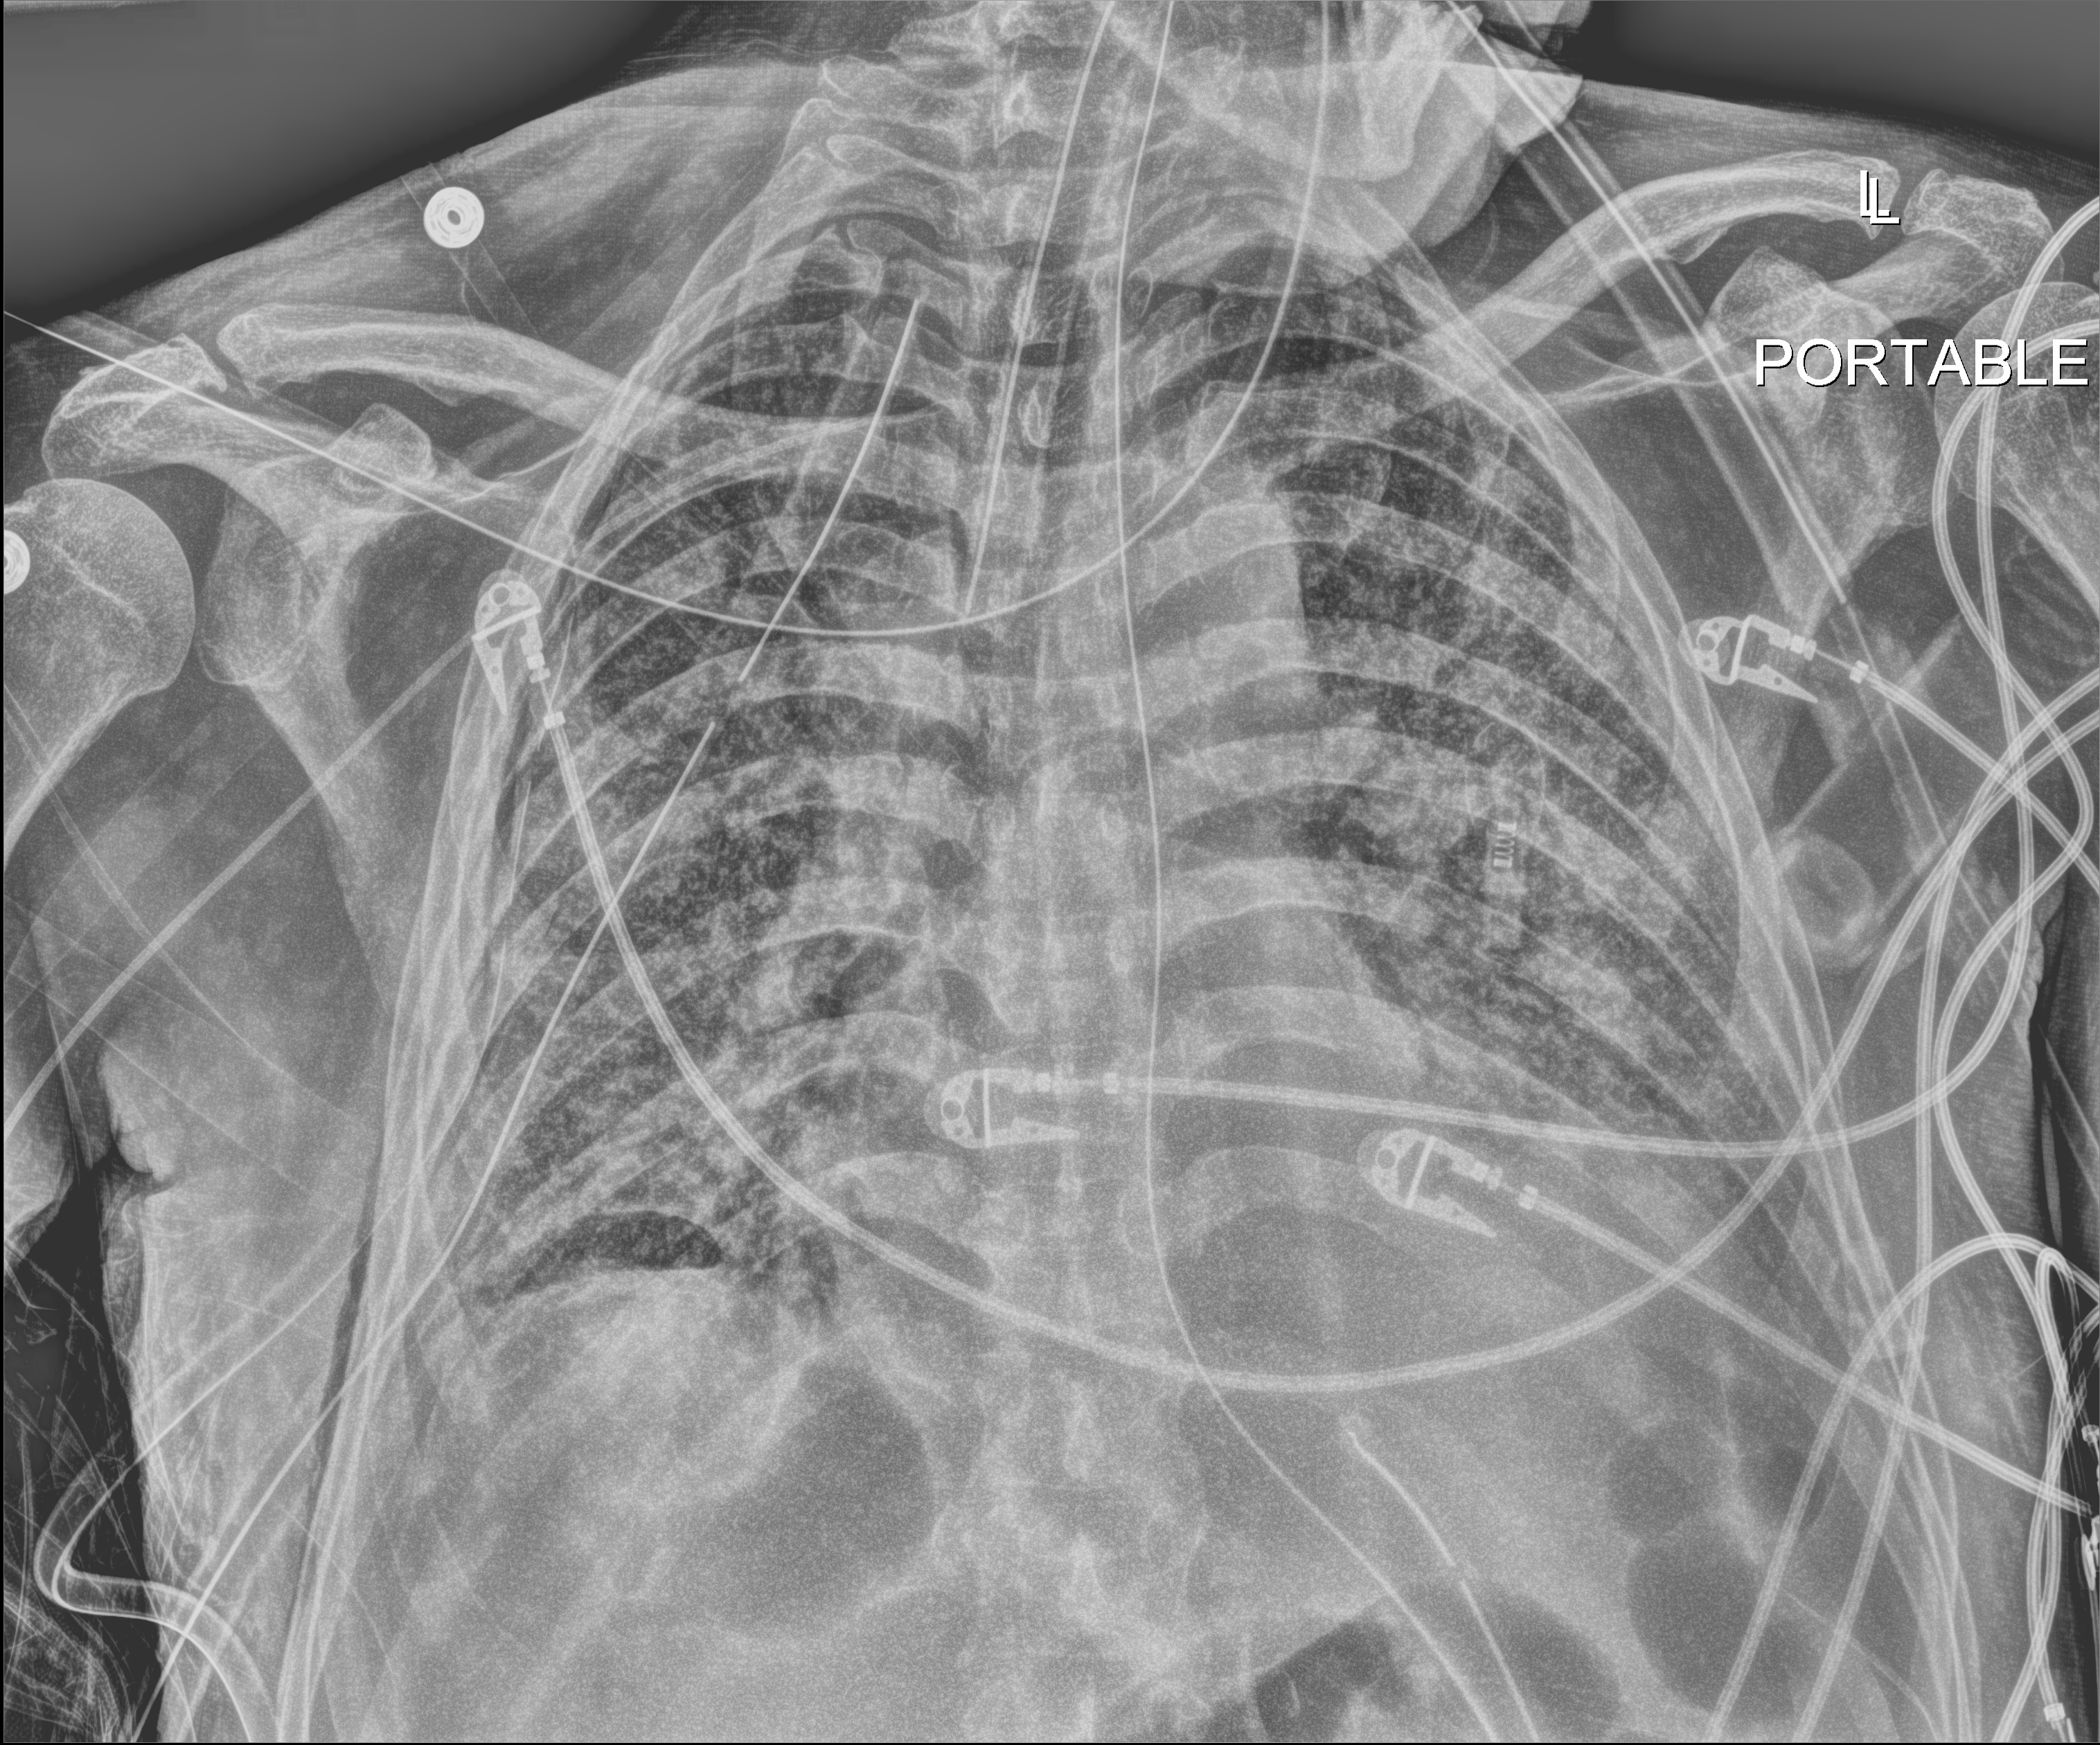
Chest radiograph. Patient hospitalised with COVID-19; male, aged 60–74 years.
Hospital-stay facts (about this admission, not read from this image; timing relative to this image not recorded): admitted to intensive care during this hospital stay: yes; mechanically ventilated during this hospital stay: yes.